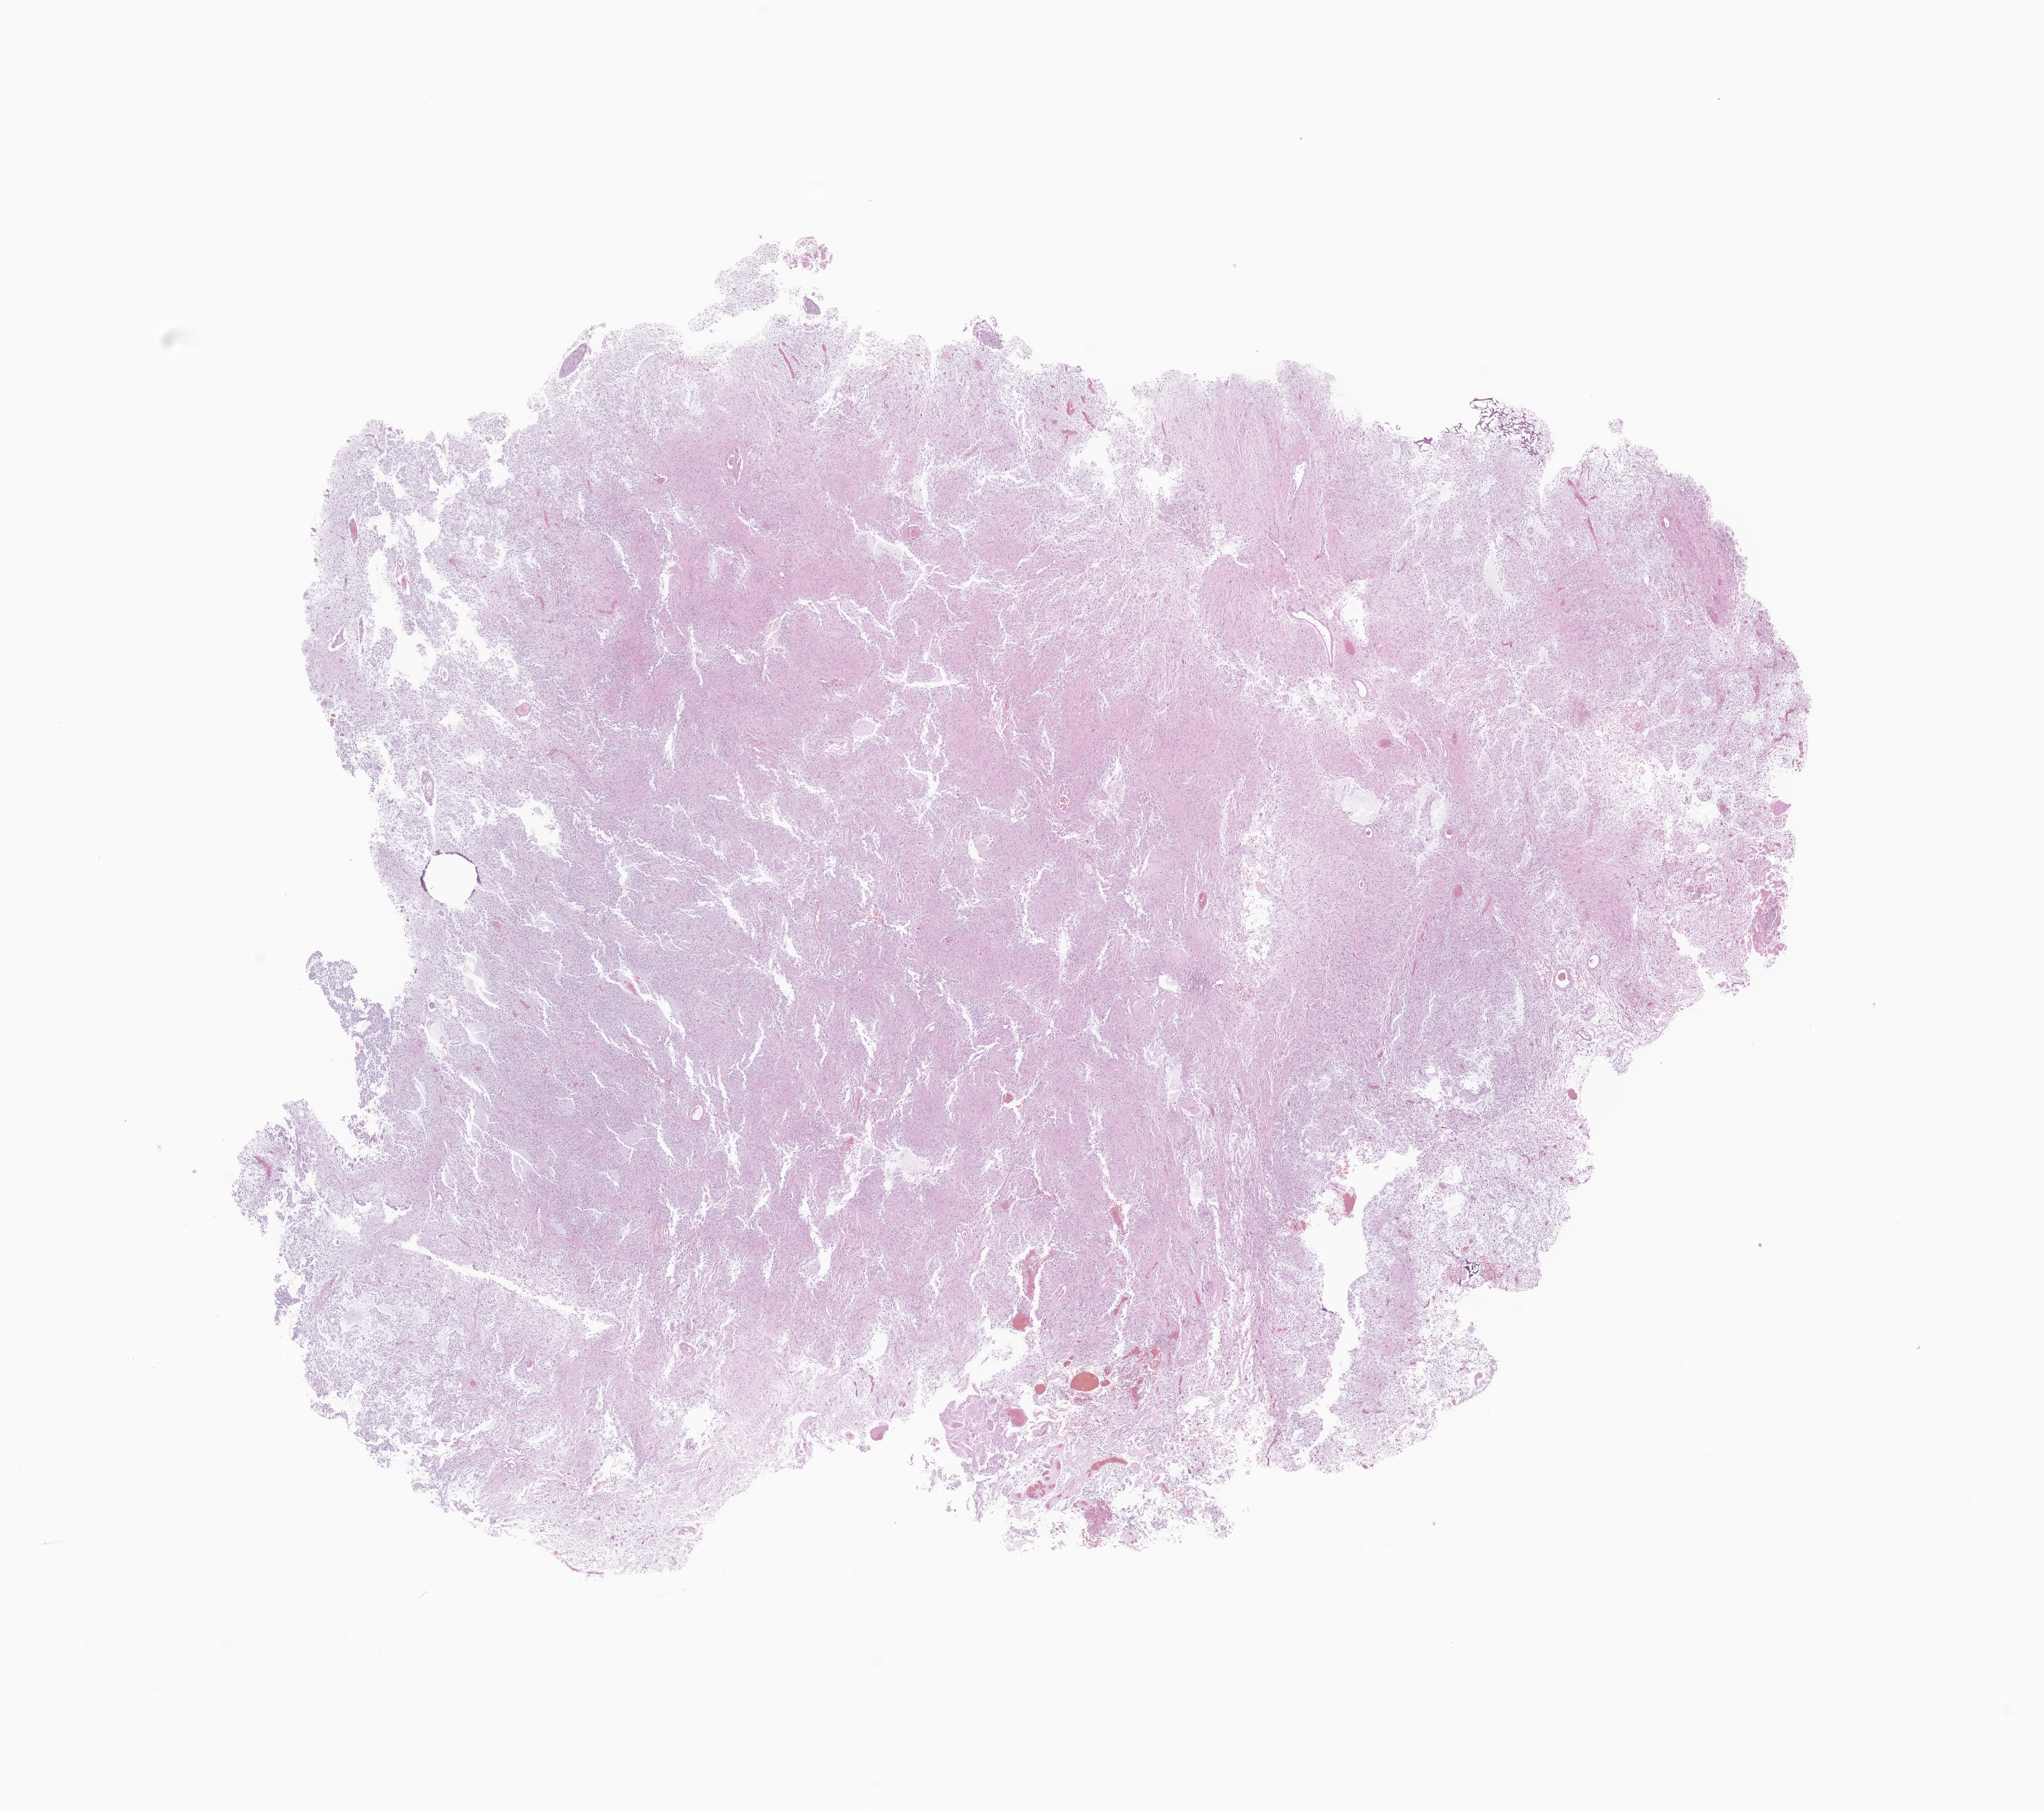
Hematoxylin and eosin (H&E) whole-slide image of tumor tissue from the brain, a low-resolution overview of the entire scanned area, about 16.2 x 14.4 mm; formalin-fixed paraffin-embedded section. Patient: male, age 65 months (5 years 5 months).
- recorded diagnosis: Pilocytic astrocytoma